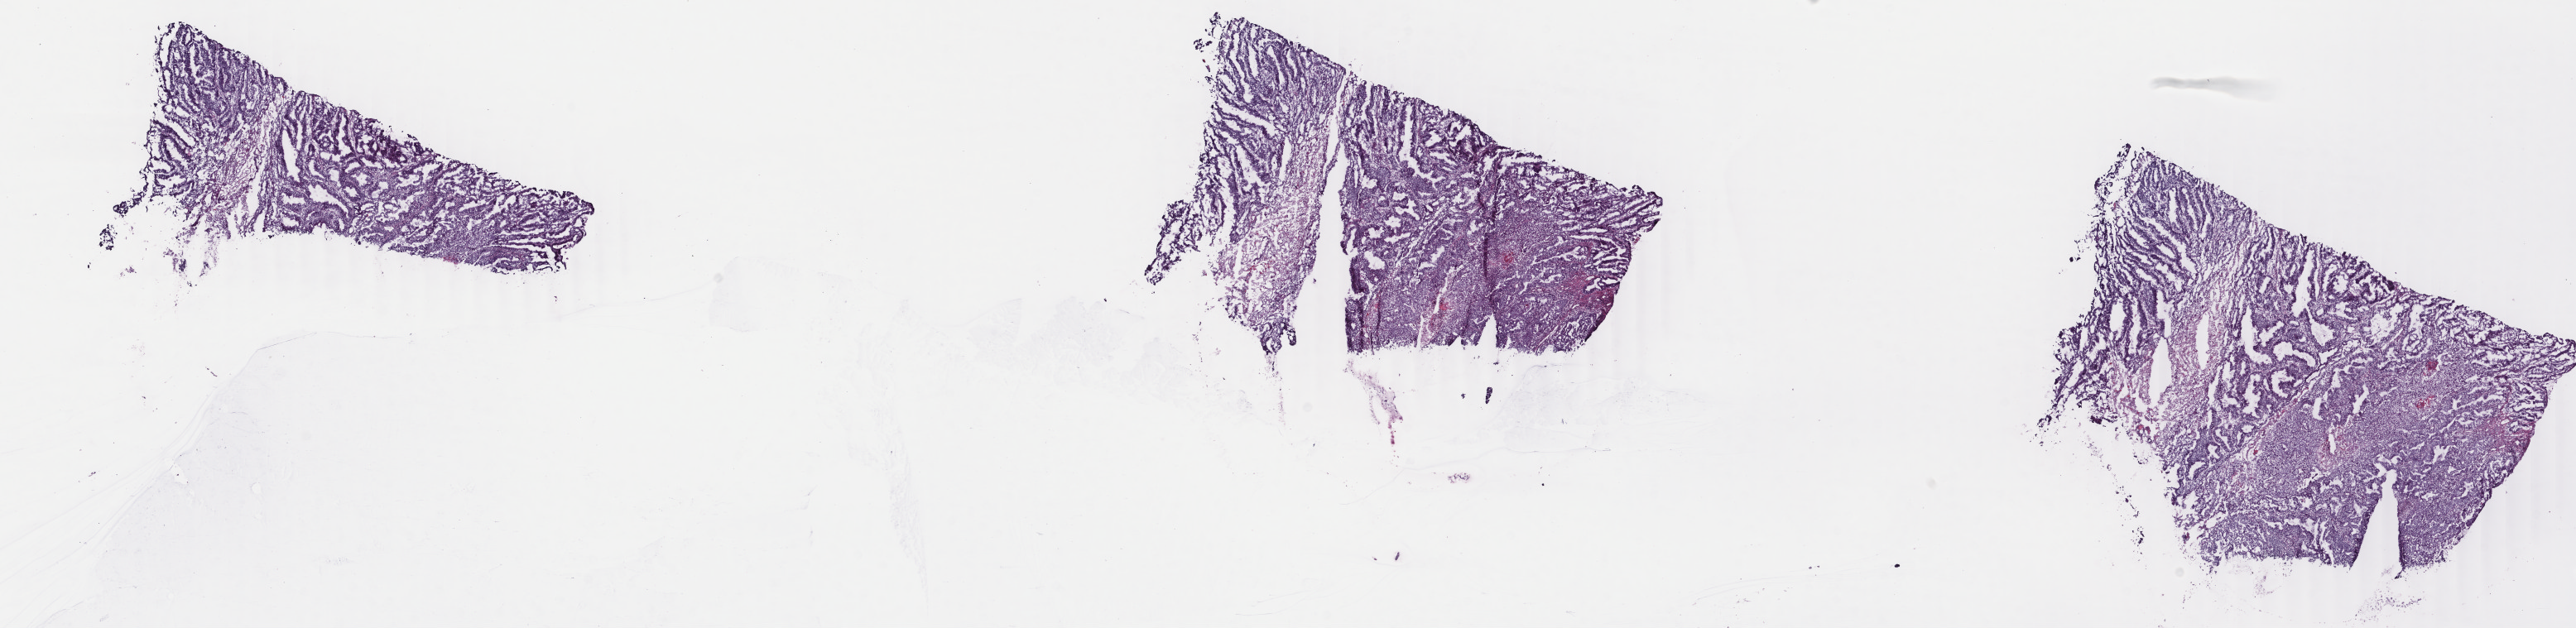
Digitized Hematoxylin and eosin (H&E) stained tissue section (whole slide) — whole scanned area (about 24.7 x 6.0 mm, from a 40x scan) shown as a low-resolution overview. Frozen section from the top of the tissue portion. Sample: primary tumour, uterus. Female, age 64 years at initial diagnosis. Histologic grade: G2 (moderately differentiated). Slide review estimates, as recorded: tumour cells 65%, tumour nuclei 70%, normal cells 0%, stromal cells 30%, necrosis 5%. Infiltration values recorded for this section: lymphocyte infiltration 2%, monocyte infiltration 2%, neutrophil infiltration 6%.
Lymph nodes positive (case pathology): 0 of 18 examined. Pathologic diagnosis: Endometrioid adenocarcinoma, NOS (endometrium). FIGO stage: IC.